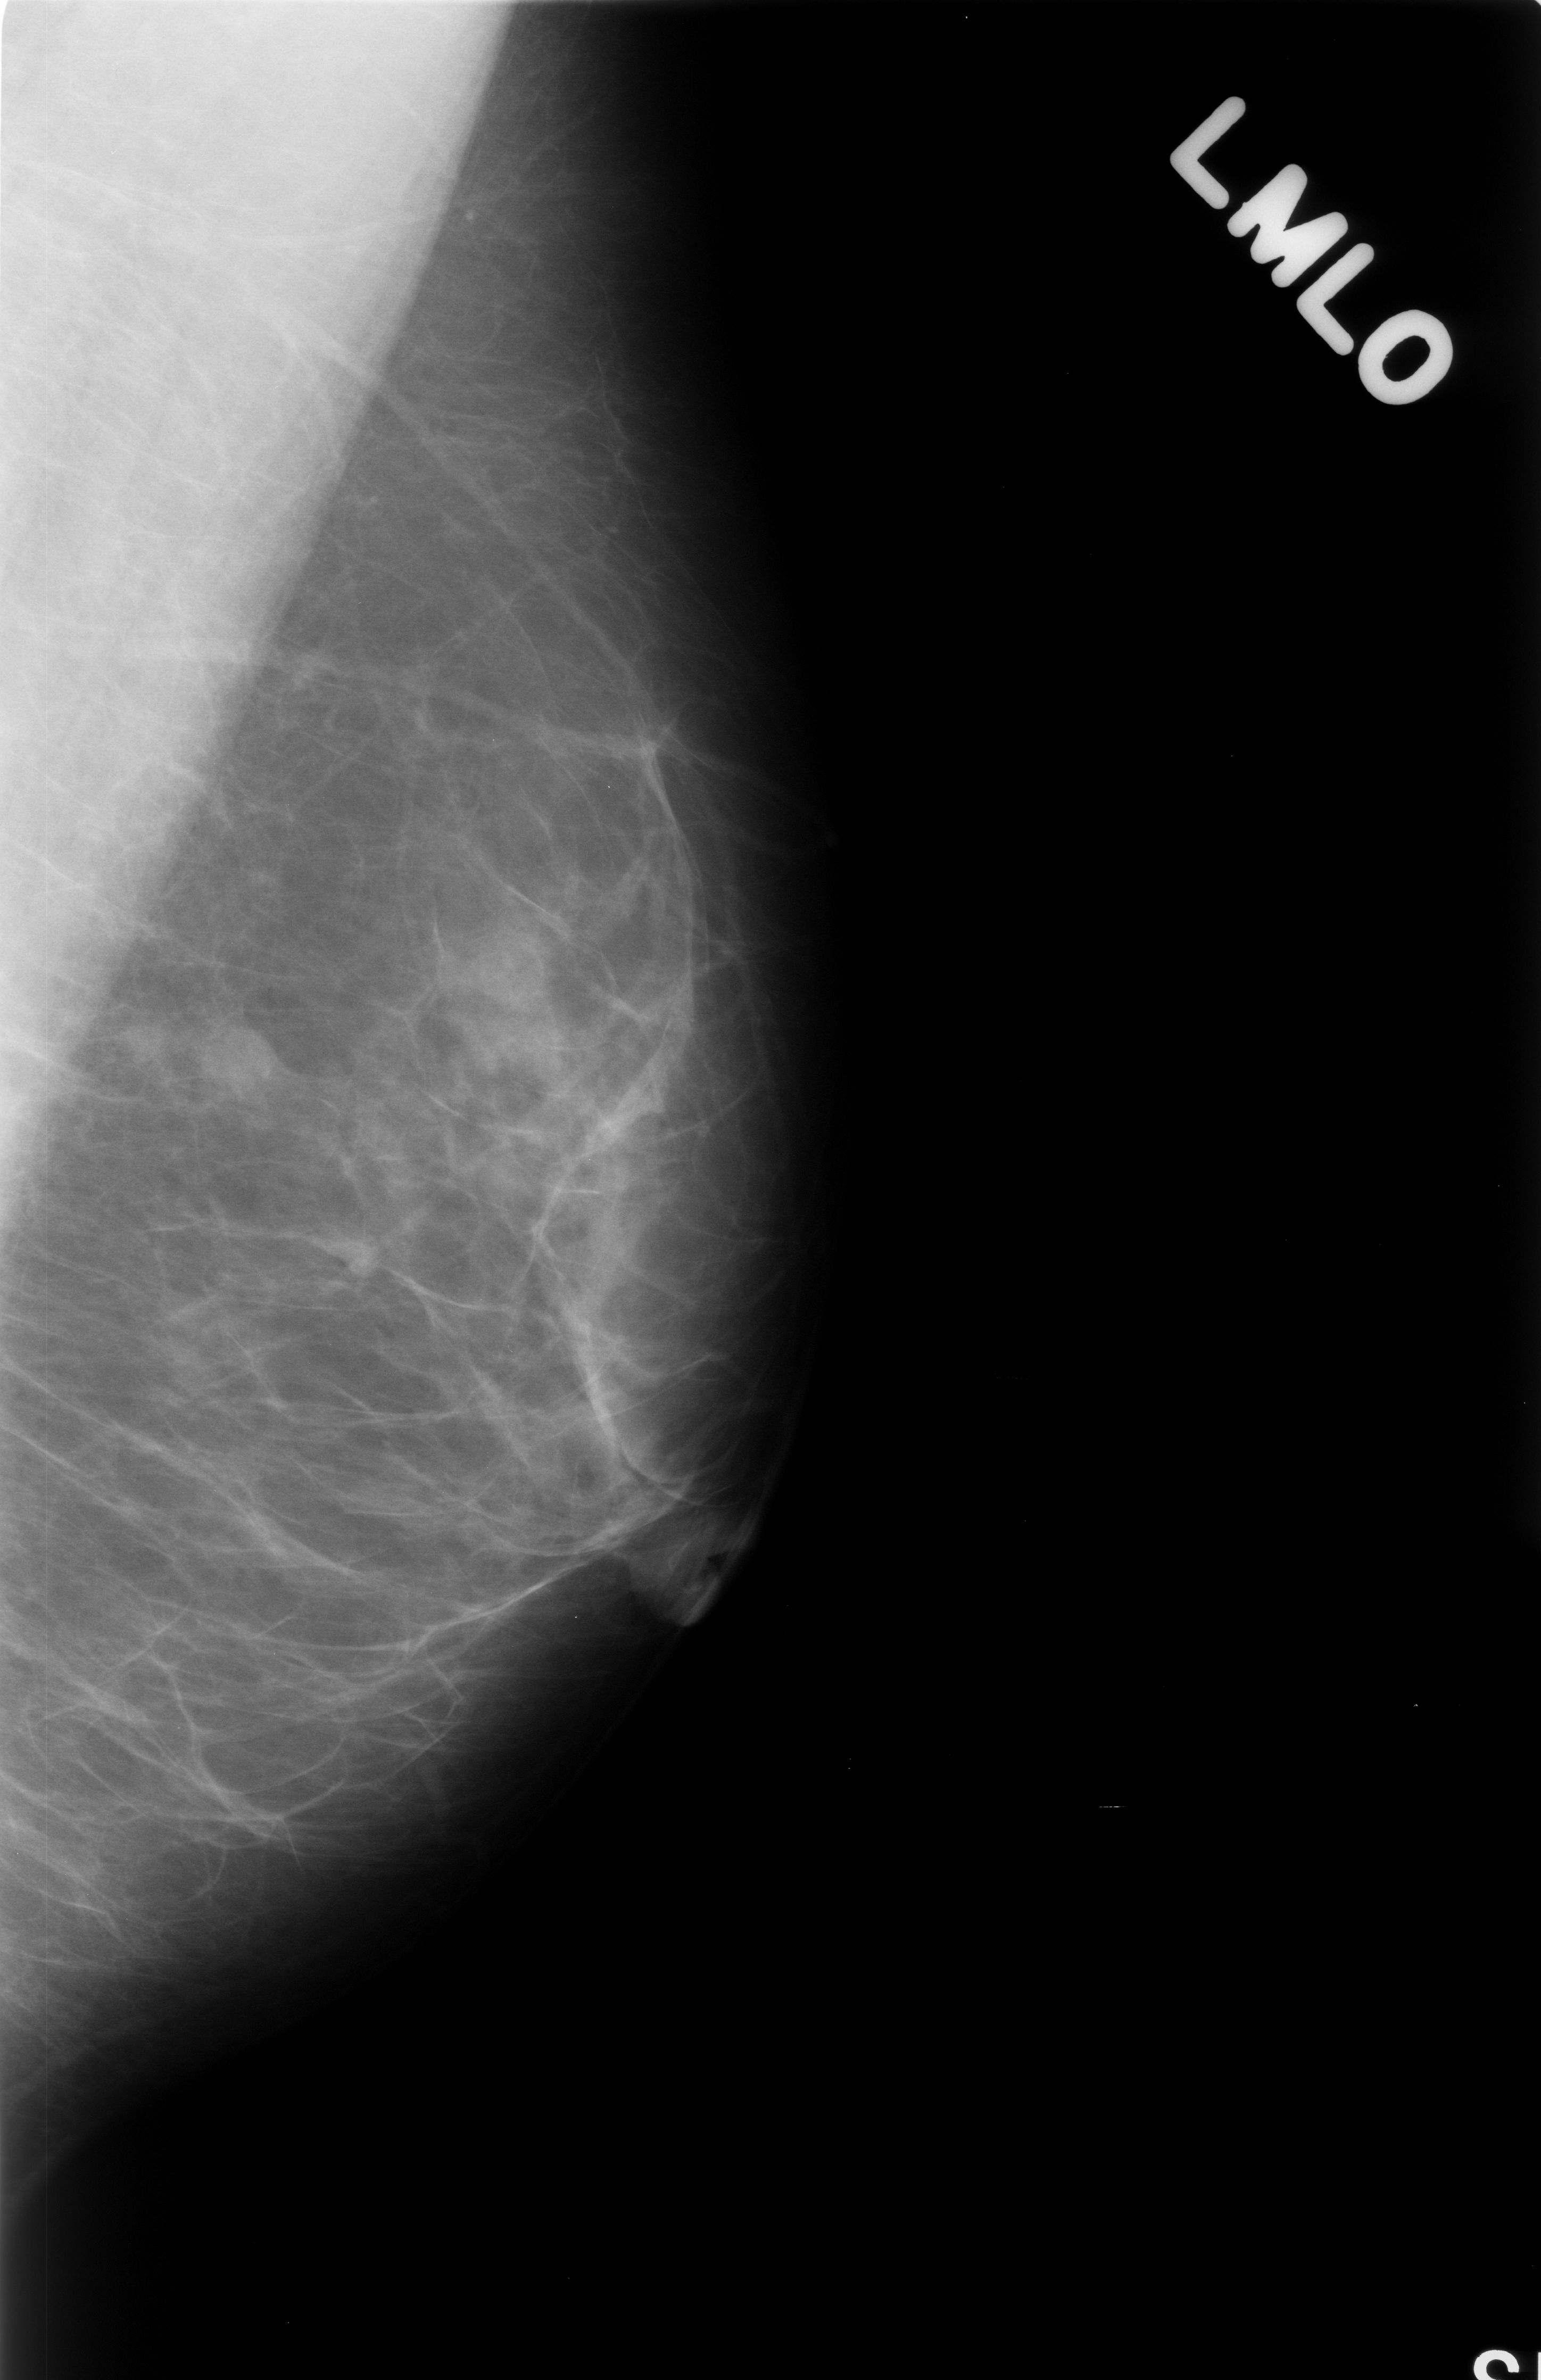
Mammogram (digitized film), left breast, mediolateral oblique (MLO) view, breast composition: almost entirely fatty (BI-RADS density category 1 of 4).
- Abnormality record for this image: mass, shape lobulated, margins circumscribed; BI-RADS assessment category 3; subtlety rating 5 on a 1 (subtle) to 5 (obvious) scale; pathology result (as recorded, not read from the image): benign.